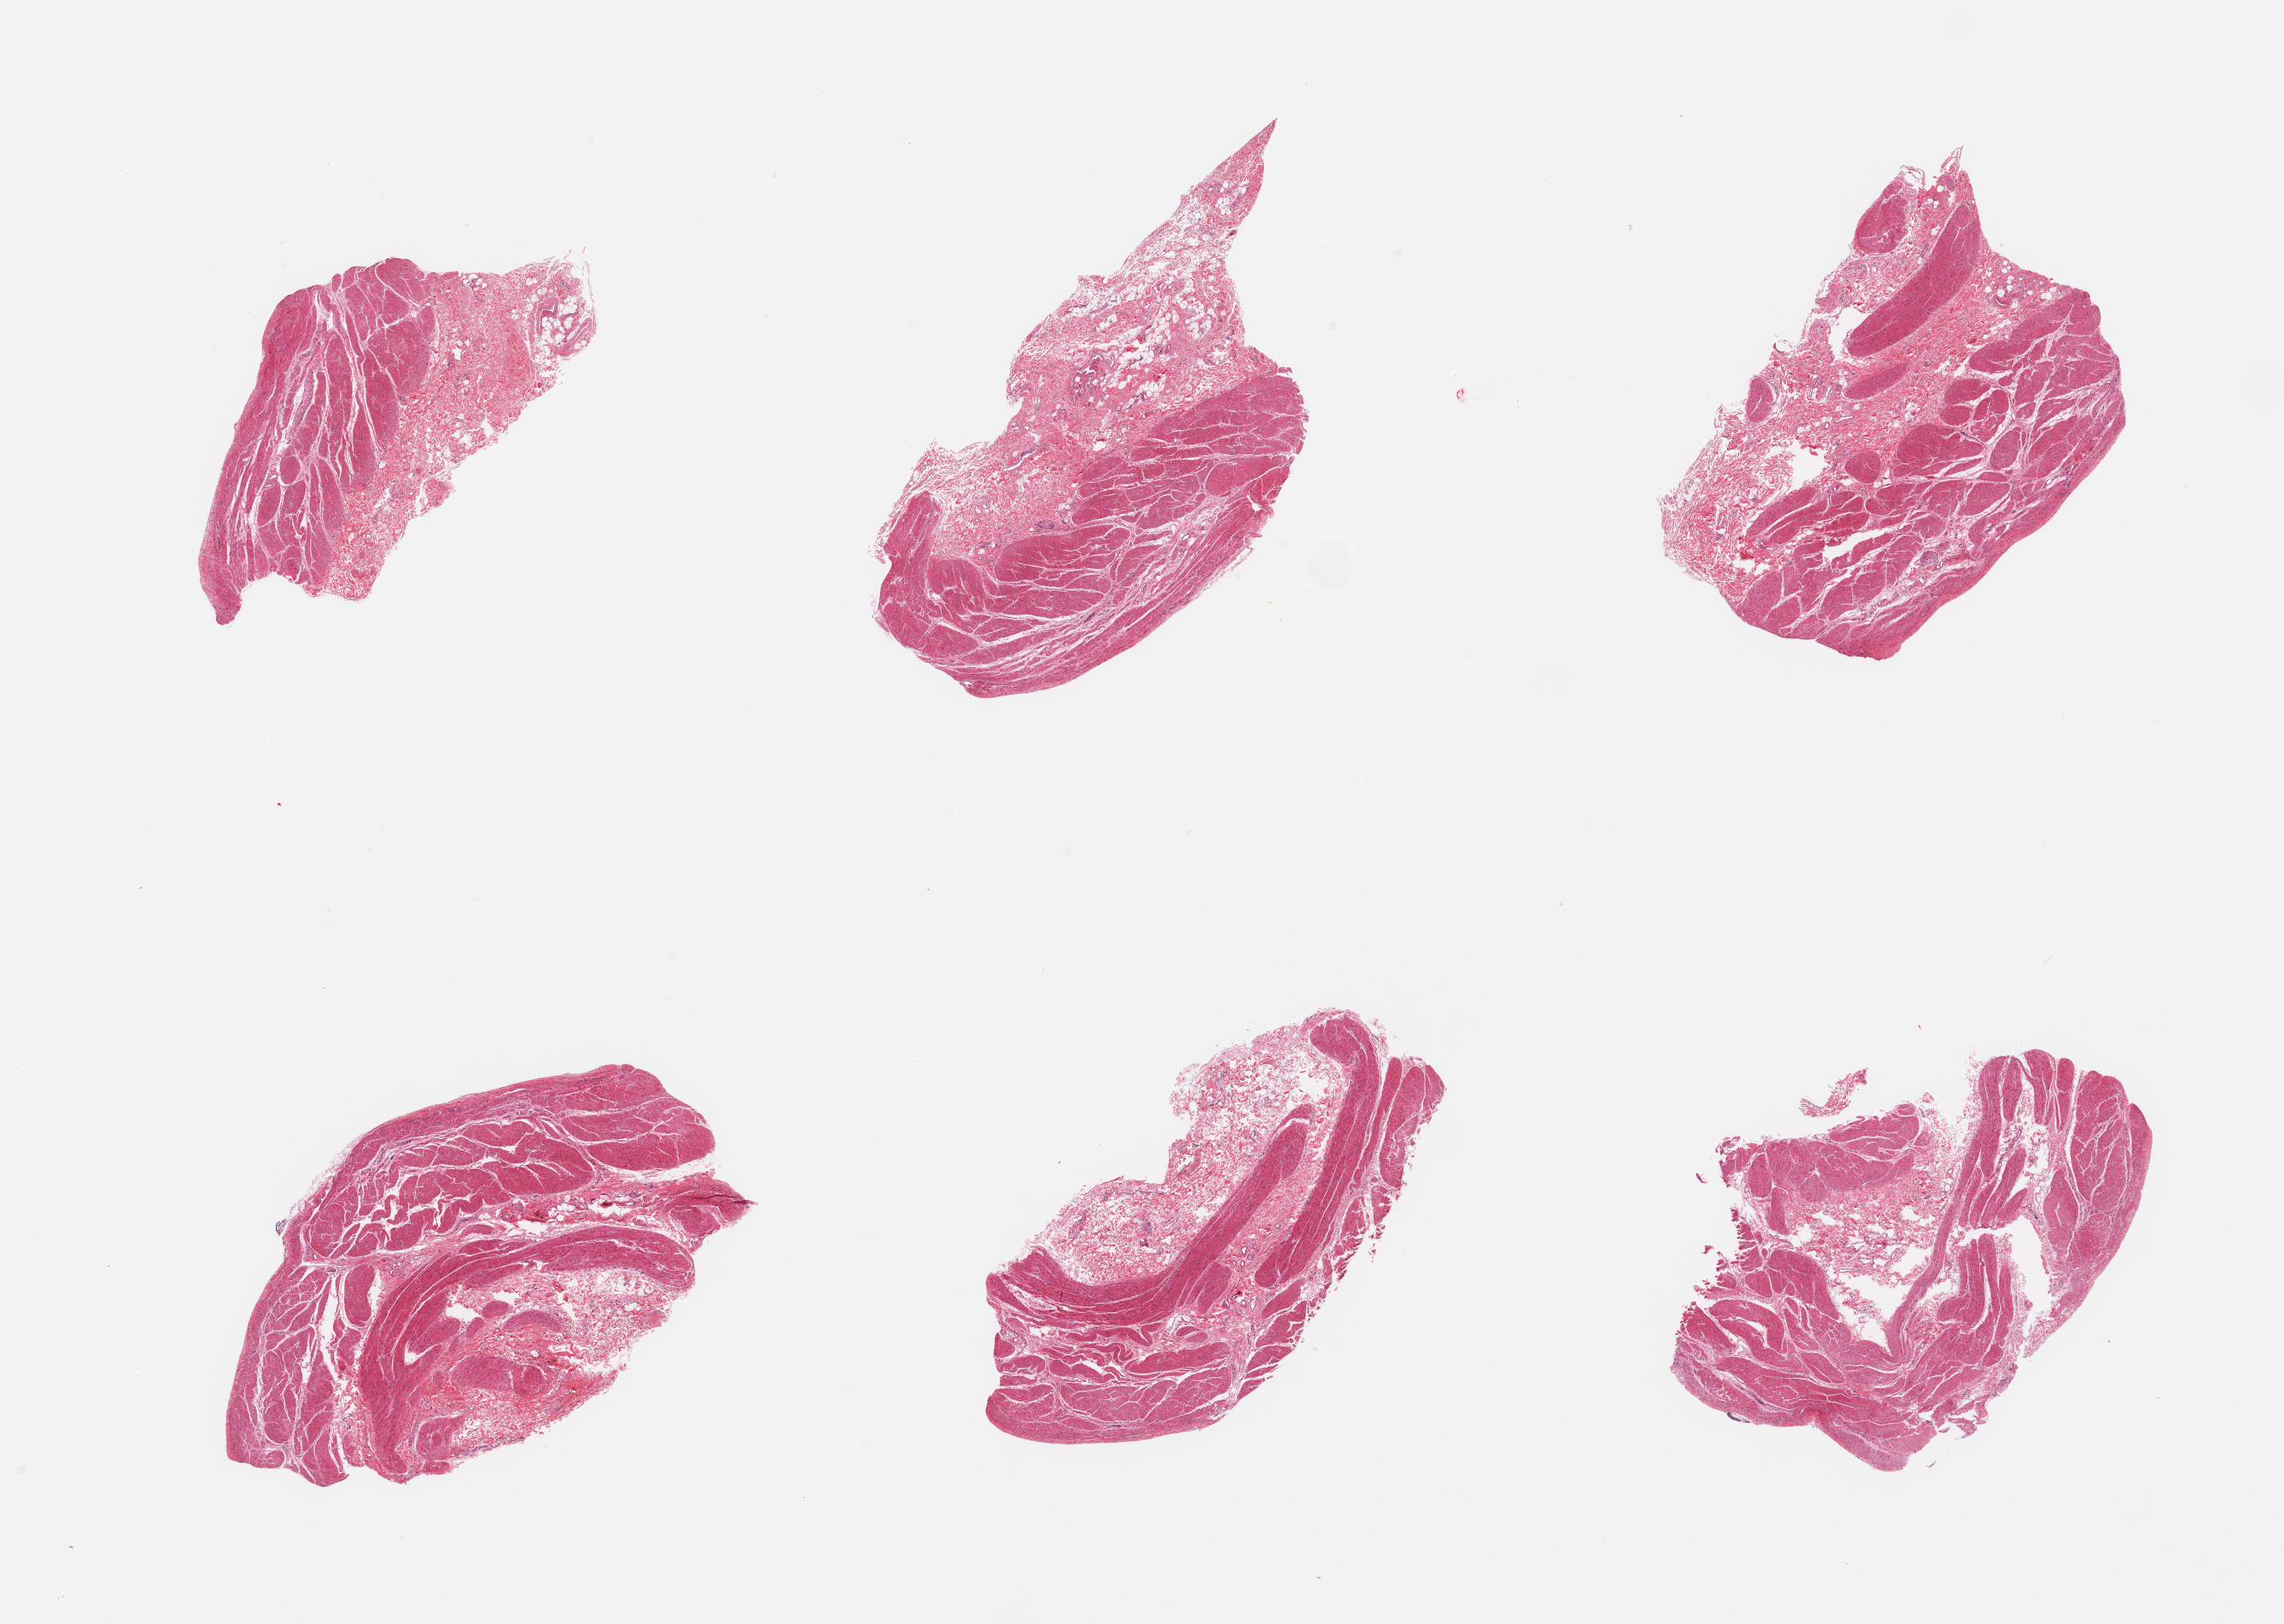
H&E whole-slide image, brightfield — a low-resolution overview of the entire scanned area, about 24.6 x 17.5 mm, PAXgene-fixed, paraffin-embedded tissue, target tissue: stomach, donor tissue sample. Donor: male.
Reviewer comment on this tissue sample: 6 pieces; muscularis, no mucosa.